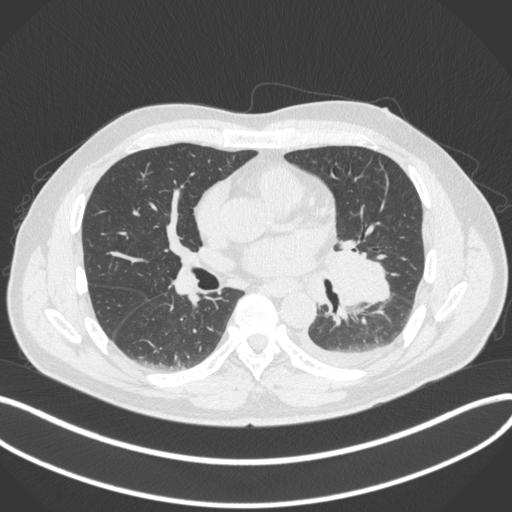
Chest CT, one axial slice; slice 185 of 350 in the series (ordered by position); reconstruction kernel B31f; 120 kVp; lung window (W 1500 / L -600 HU); 1 mm slice thickness; 512 × 512 image matrix, field of view 400 × 400 mm. Patient: male, 58 years. From the clinical record (not read from this slice): clinical TNM (as recorded): T3 N1 M1b; histopathological grade: G3.
Outlined on this slice (rectangle marked by the reading radiologist):
- lung tumour (recorded histology: small cell carcinoma): box from (x=323, y=243) to (x=391, y=303) px